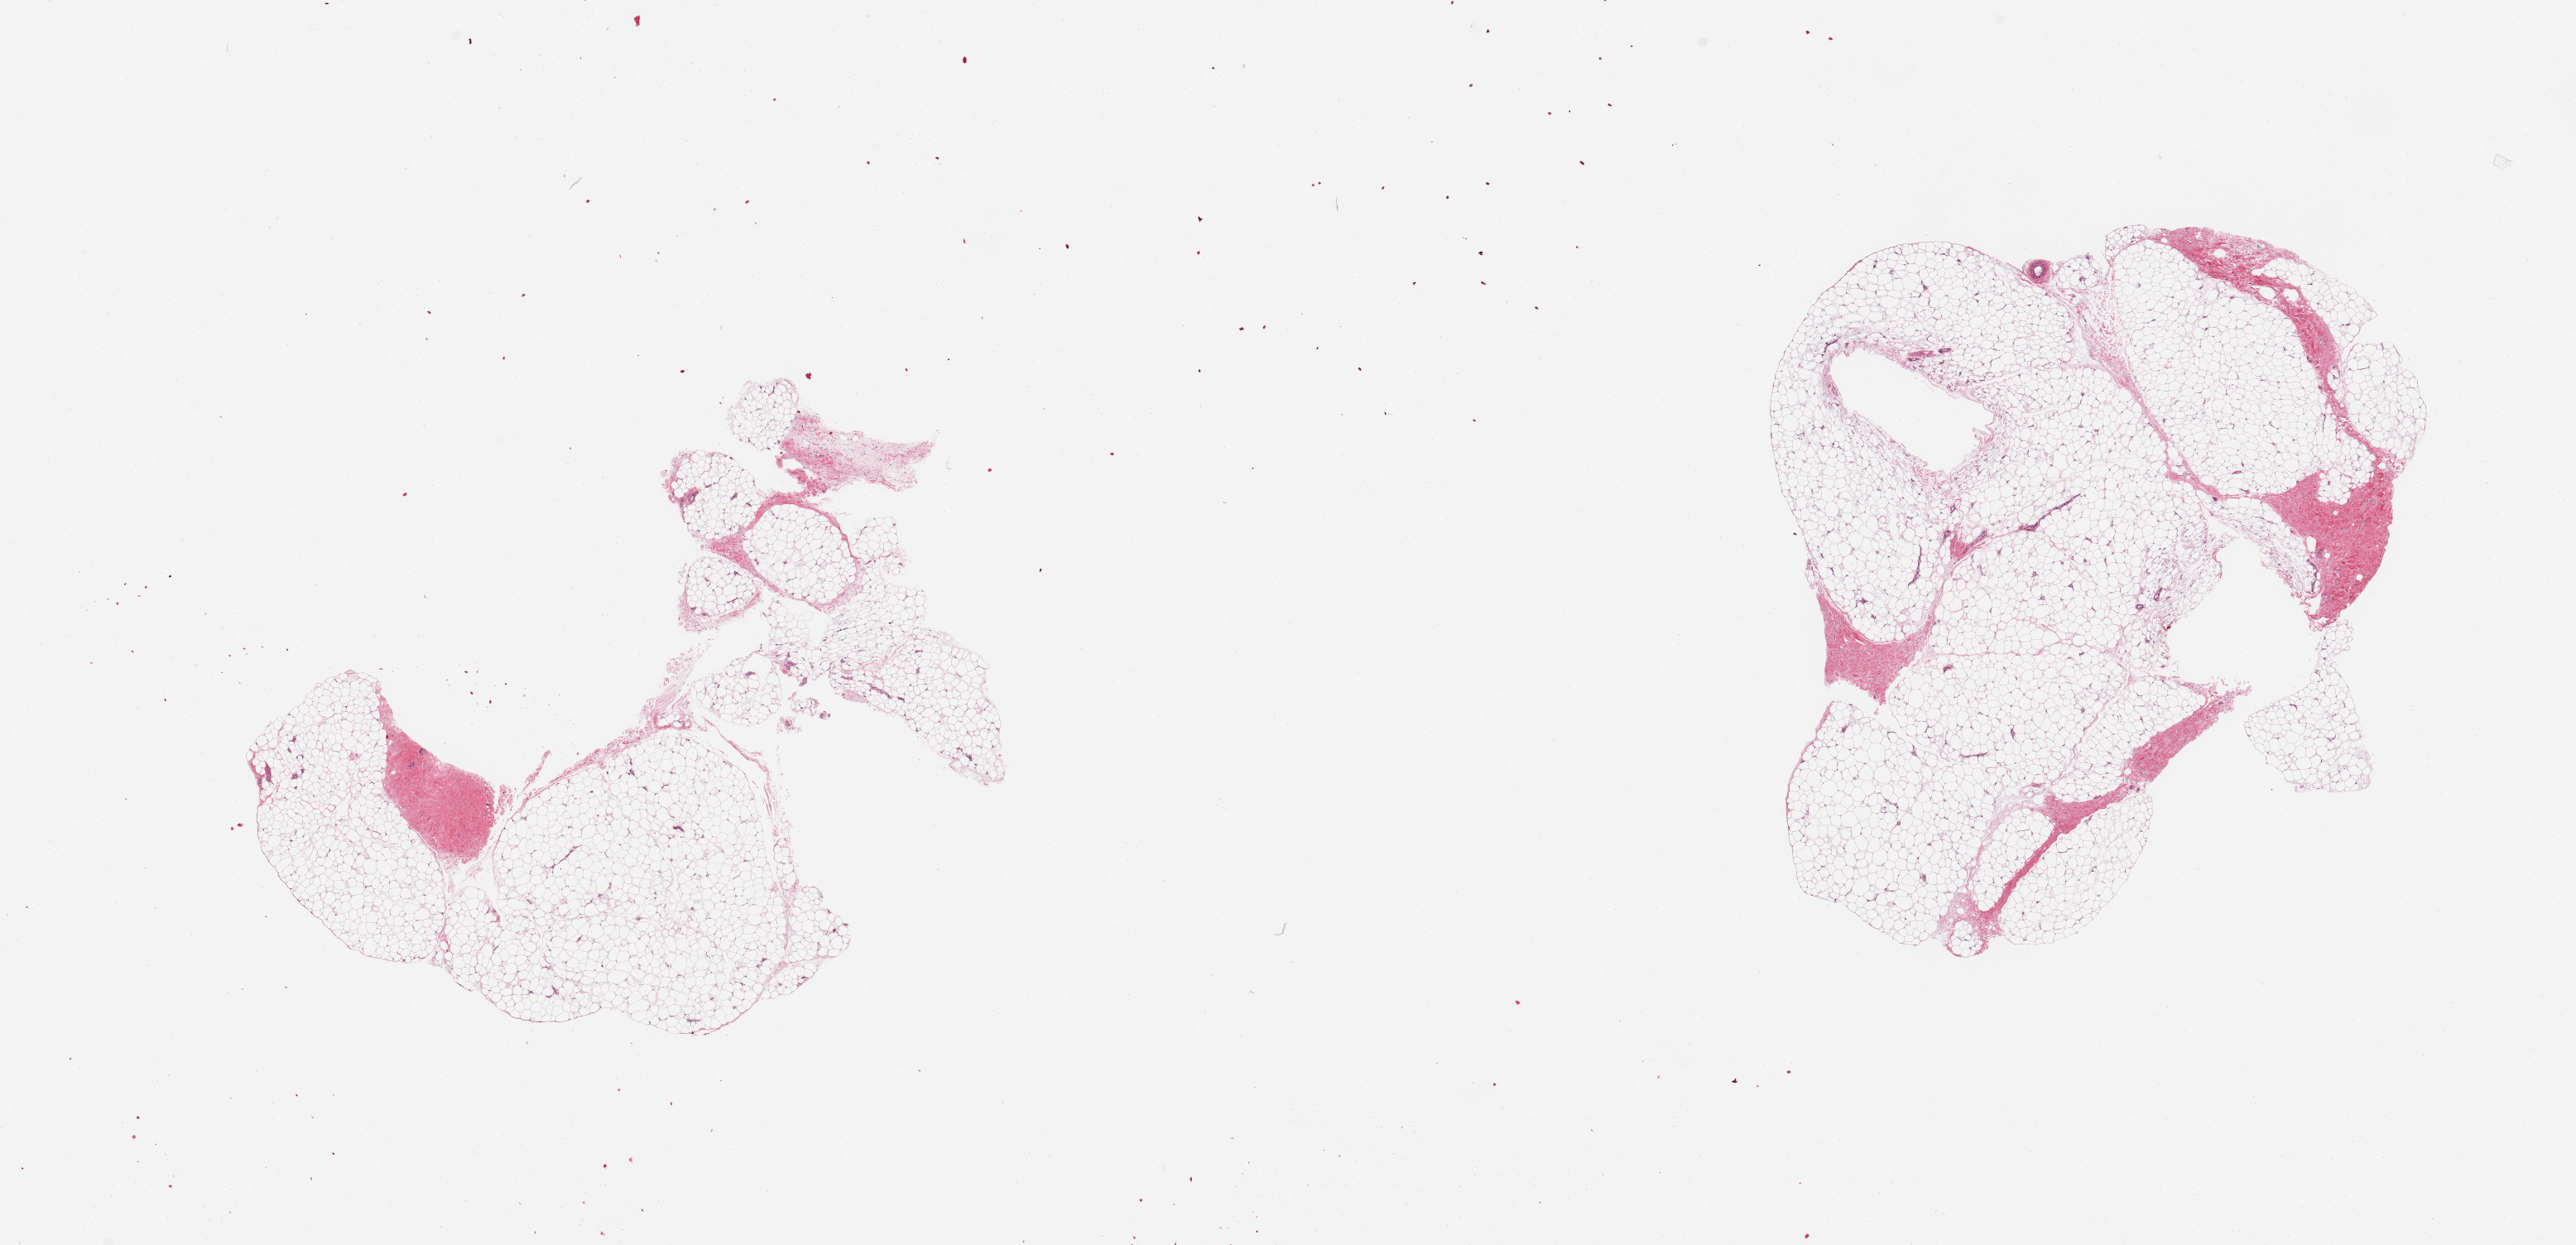
Digitized haematoxylin and eosin-stained section, shown as a low-resolution overview of the whole scanned area (about 24.6 x 11.9 mm), PAXgene-fixed, paraffin-embedded tissue, target tissue: adipose tissue, donor tissue sample.
Reviewer comment on this tissue sample: 2 pieces; <5% fibrous content.